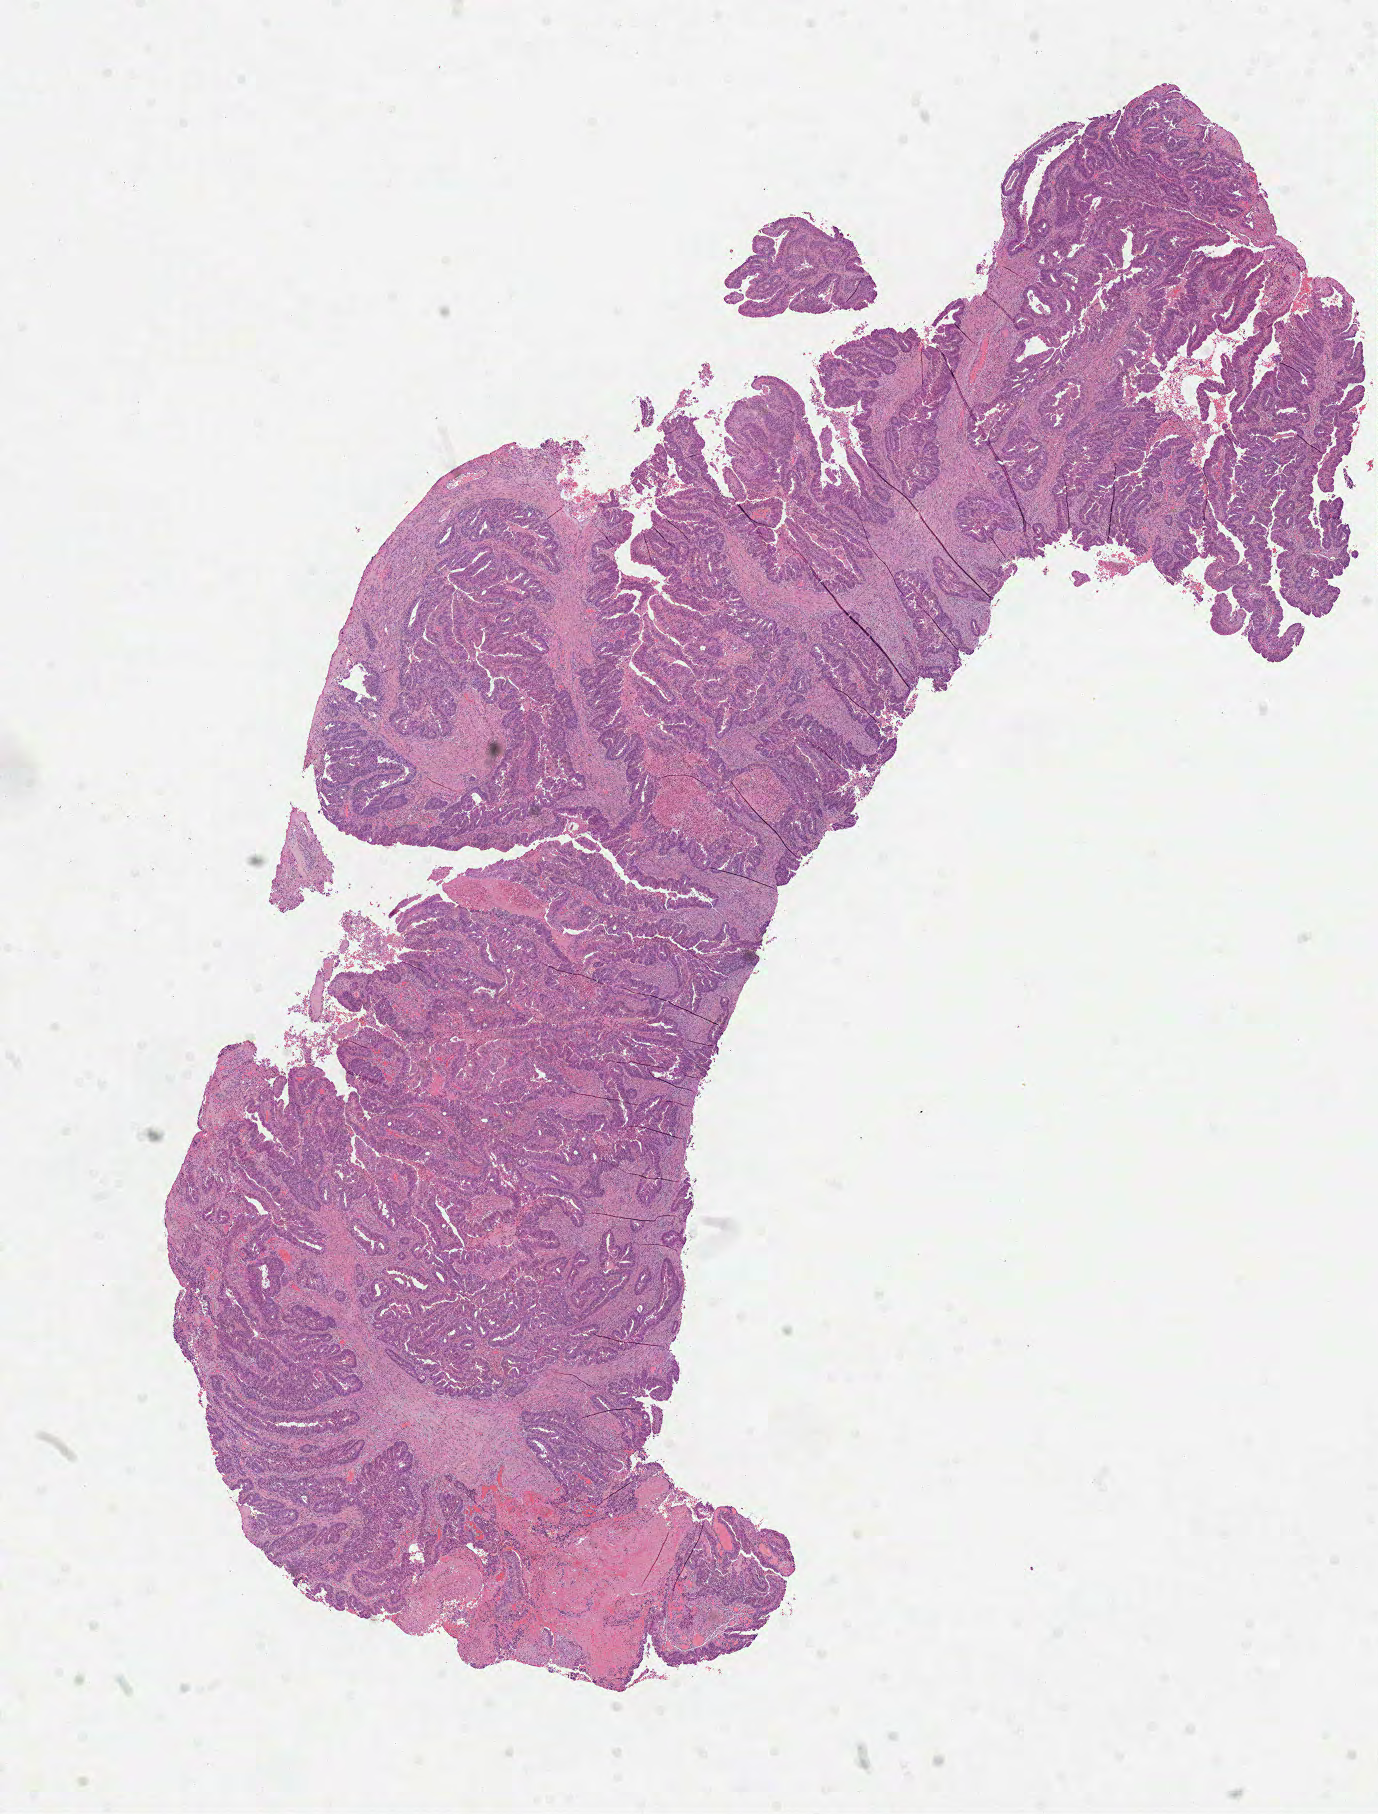
H&E whole-slide image — whole scanned area (about 11.1 x 14.6 mm, acquisition: 40x scan) shown as a low-resolution overview, formalin-fixed paraffin-embedded (FFPE) diagnostic section, sample: primary tumour, rectum. Patient: male, age at initial diagnosis 66 years.
- pathologic diagnosis: Adenocarcinoma, NOS